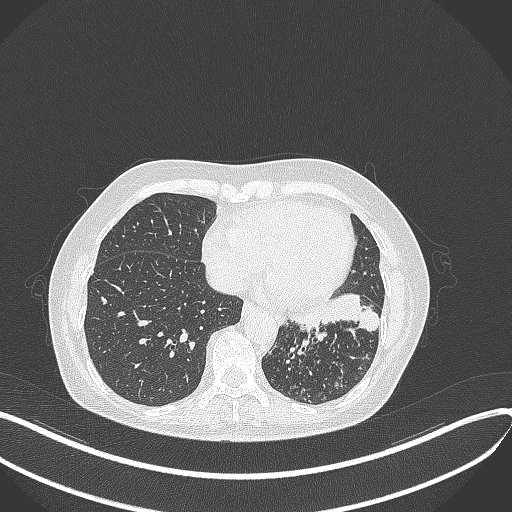
Chest CT, one axial slice; position 136 of 429 along the scan axis; reconstruction kernel B70f; lung window (W 1500 / L -600 HU); 1 mm slice thickness; 512 × 512 image matrix, field of view 400 × 400 mm. Female patient, age 63 years. Case-level facts recorded for this patient, not image findings: clinical TNM (as recorded): T1b N0 M0.
Annotated regions visible in this slice (bounding box drawn by a radiologist):
- lung tumour (recorded histology: adenocarcinoma): bounding box (x1, y1, x2, y2) in pixels: (285, 284, 380, 343)